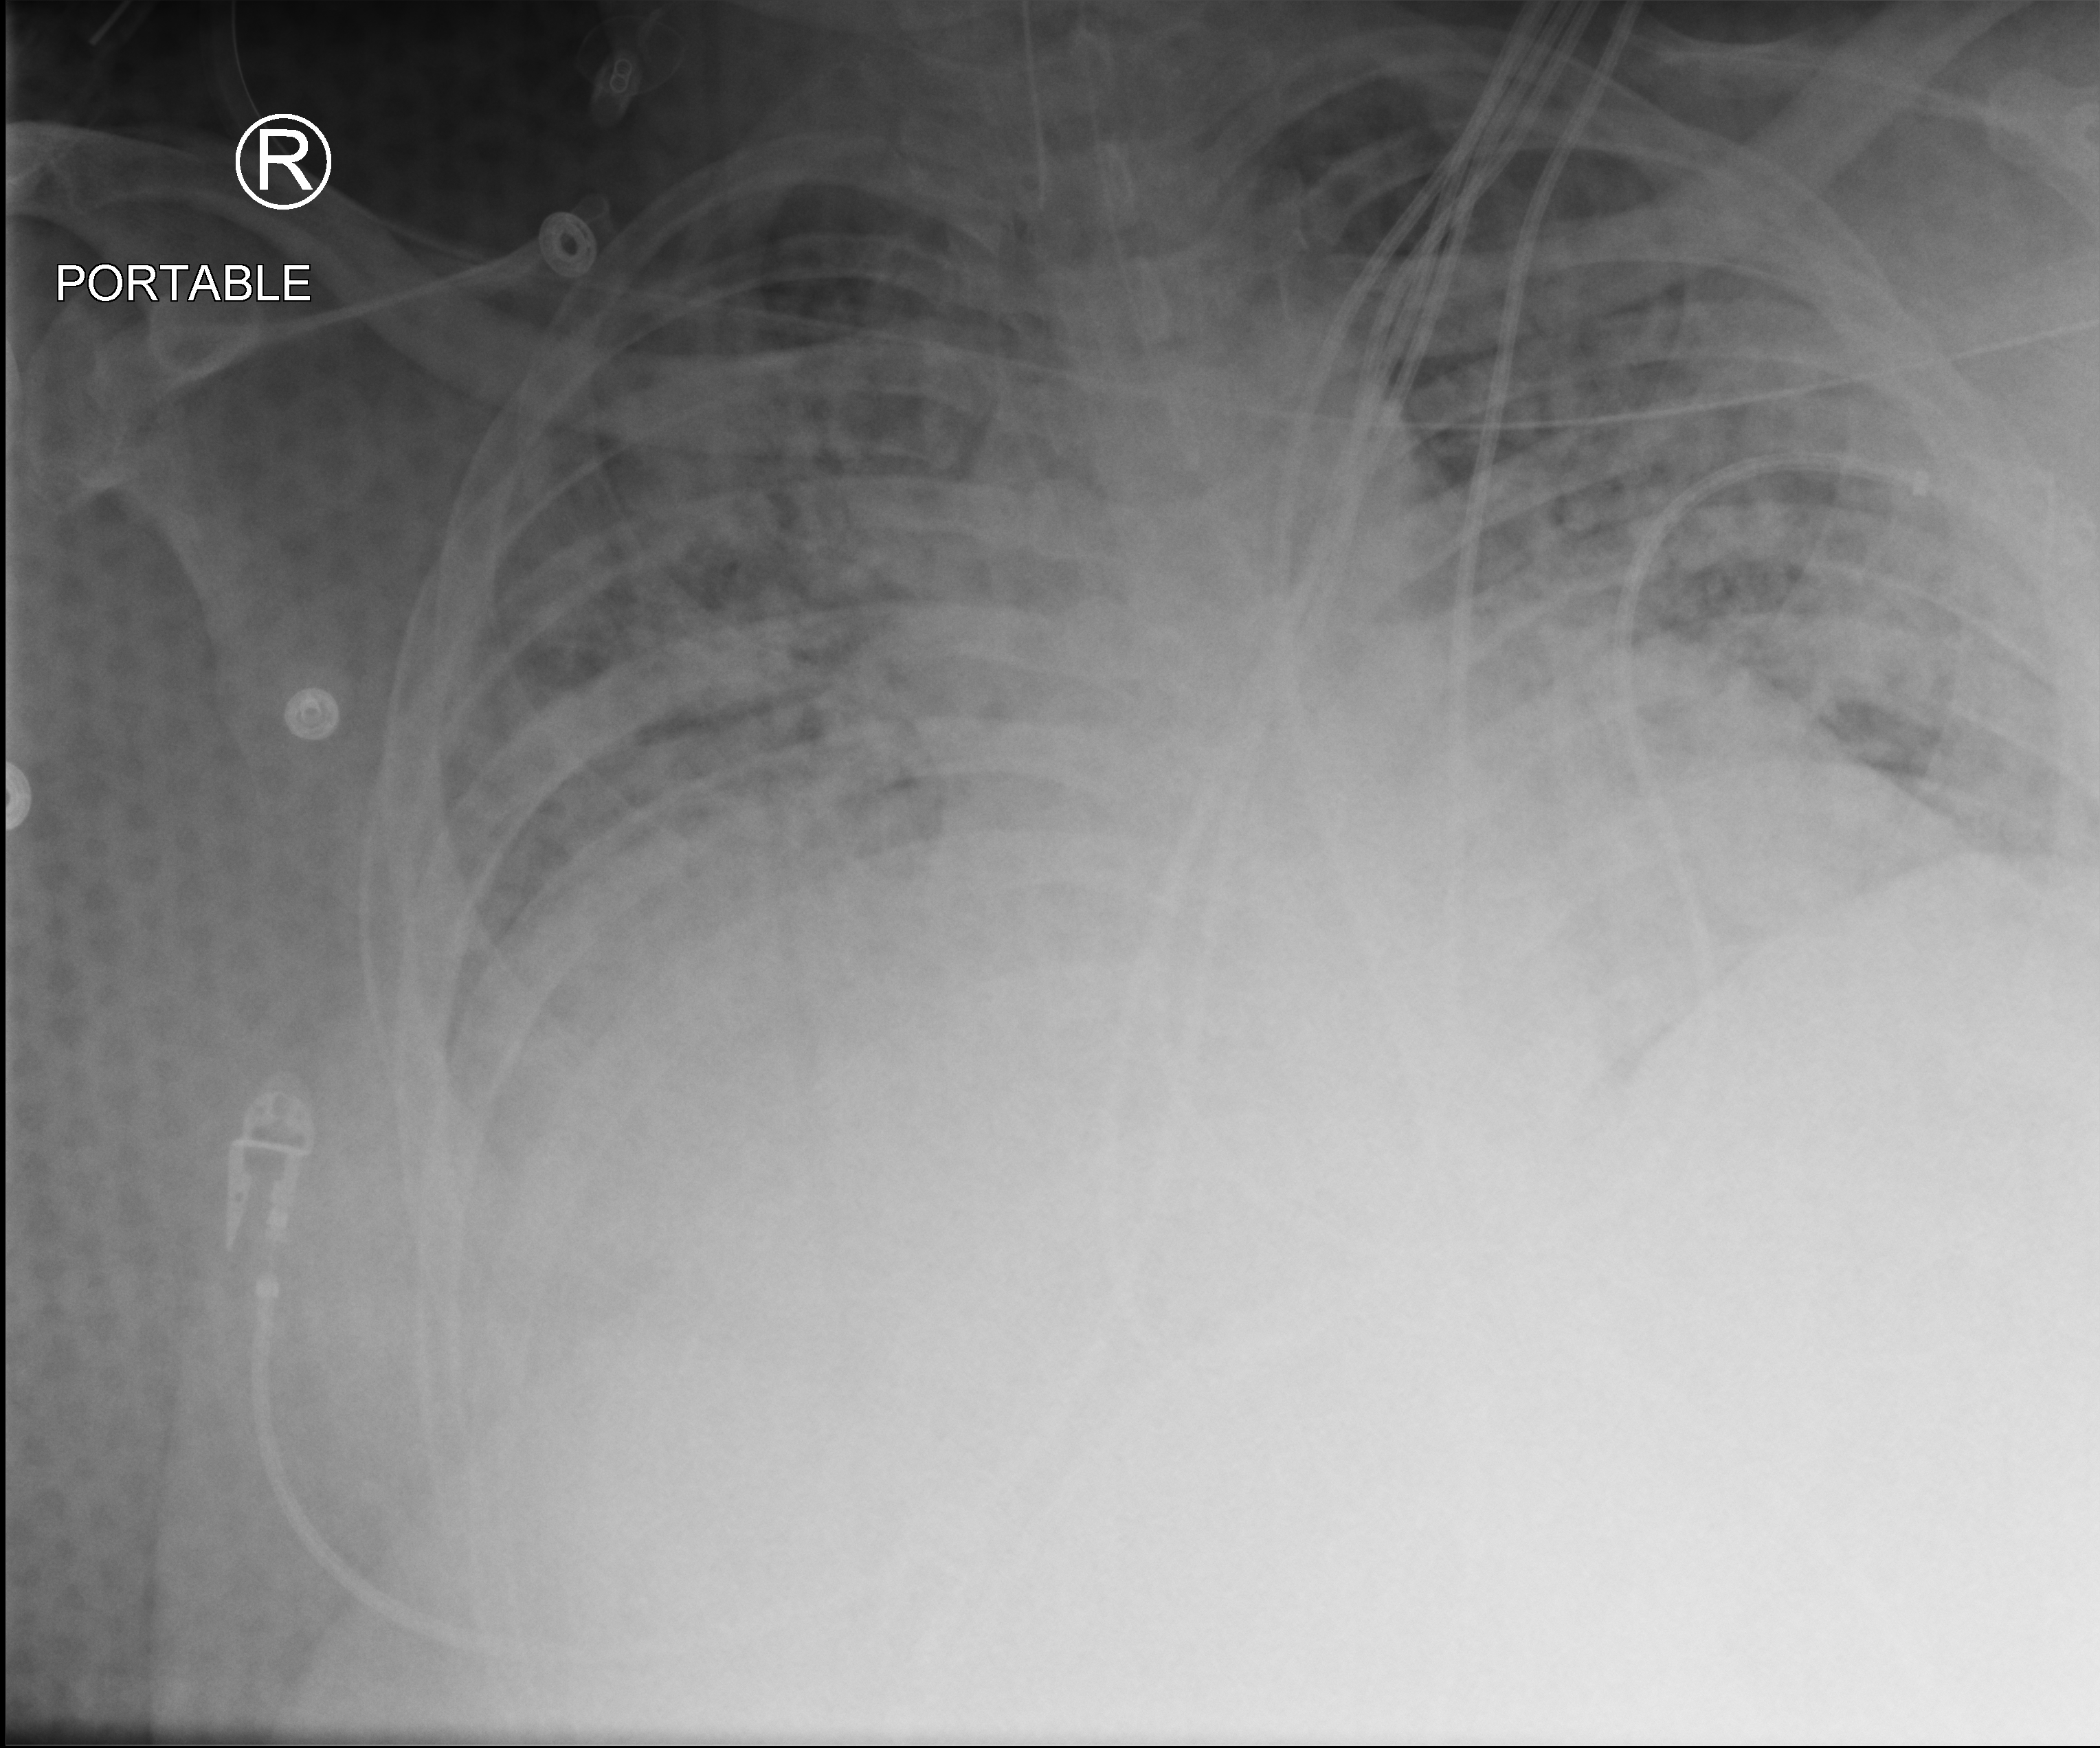
Bedside chest radiograph (computed radiography); anteroposterior (AP) projection. Male patient hospitalised with COVID-19, age 18–59 years.
Hospital-stay facts (about this admission, not read from this image; timing relative to this image not recorded): diabetes (admission record): yes; mechanically ventilated during this hospital stay: yes.